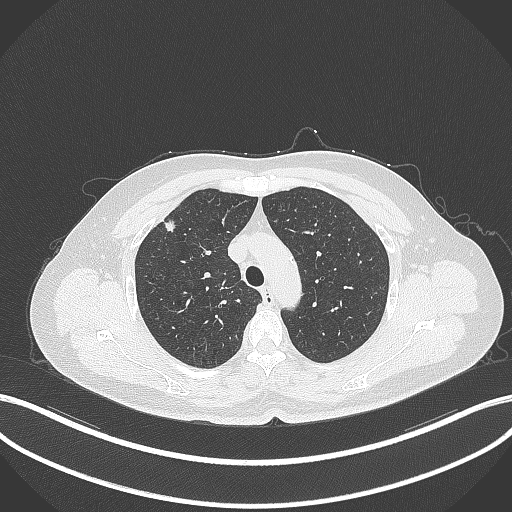
Chest CT, one axial slice. Position 278 of 353 along the scan axis. Reconstruction kernel B70f. 120 kVp. Lung window (W 1500 / L -600 HU). 512 × 512 image matrix, field of view 400 × 400 mm. Female patient, age 56 years. Case-level facts recorded for this patient, not image findings: clinical TNM (as recorded): T1c N0 M0.
Annotated regions visible in this slice (rectangle marked by the reading radiologist):
- lung tumour (recorded histology: adenocarcinoma): box from (x=159, y=214) to (x=178, y=234) px